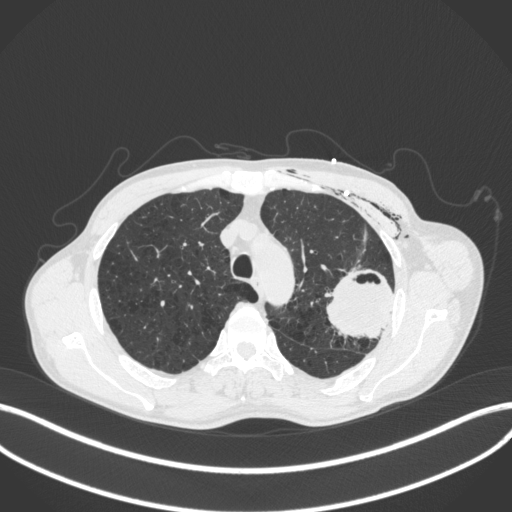
Chest CT, one axial slice. Position 306 of 416 along the scan axis. Reconstruction kernel B31f. 120 kVp. Lung window (W 1500 / L -600 HU). 1 mm slice thickness. 512 × 512 image matrix, field of view 400 × 400 mm. Patient: male, 58 years. From the clinical record (not read from this slice): clinical TNM (as recorded): T3 N0 M0.
Outlined on this slice (rectangle marked by the reading radiologist):
- lung tumour (recorded histology: adenocarcinoma): bounding box (x1, y1, x2, y2) in pixels: (321, 267, 403, 346)